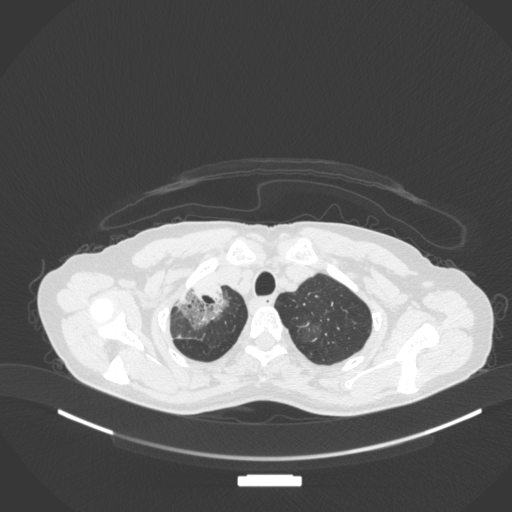
Chest CT, one axial slice. Position 285 of 311 along the scan axis. Reconstruction kernel B31f. 120 kVp. Lung window (W 1500 / L -600 HU). 1 mm slice thickness. 512 × 512 image matrix, field of view 400 × 400 mm. Patient: female, 59 years. From the clinical record (not read from this slice): clinical TNM (as recorded): T3 N0 M0; histopathological grade: G1.
Structures marked on this image (bounding box drawn by a radiologist):
- lung tumour (recorded histology: adenocarcinoma): bounding box <172,276,231,330> (left, top, right, bottom; pixels)